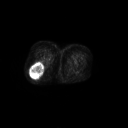
FDG PET of an extremity soft-tissue mass (from a PET/CT study), one axial slice; position 36 of 267 along the scan axis; 3.27 mm slice thickness; 128 × 128 image matrix, field of view 700 × 700 mm. Patient: female, 70 years. Case-level facts recorded for this patient, not image findings: histological type: synovial sarcoma; grade: intermediate; site of the primary tumour: right buttock.
Outlined on this slice (expert contour drawn on MRI and transferred to this co-registered scan by the dataset authors):
- gross tumour volume including surrounding oedema: bounding box (x1, y1, x2, y2) in pixels: (29, 61, 44, 78)
- gross tumour volume (mass): (29, 62, 44, 78)